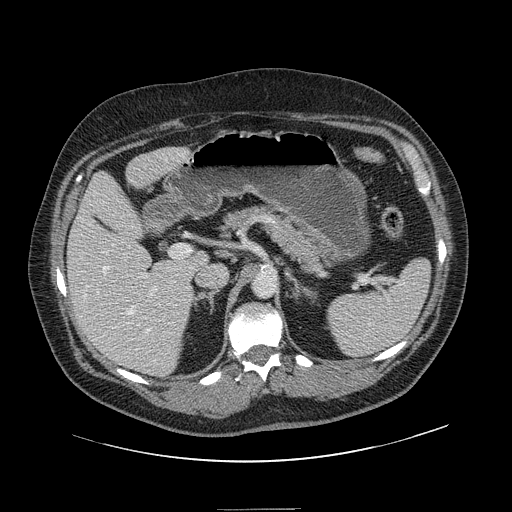
Contrast-enhanced abdominal CT, one axial slice; 120 kVp; intravenous contrast given; soft-tissue window (W 400 / L 40 HU); 2.5 mm slice thickness; 512 × 512 image matrix. Male patient, age 61 years. Case-level facts recorded for this patient, not image findings: diagnosis: colorectal cancer liver metastases, imaged before liver resection; multiple liver metastases: yes; largest metastasis: 2.6 cm.
Outlined on this slice (outlined manually by an expert reader):
- hepatic veins: bounding box <103,244,155,362> (left, top, right, bottom; pixels)
- liver: <68,147,206,376>
- planned liver remnant (the part of the liver to remain after resection): <70,149,207,366>
- portal vein (with intrahepatic branches): <96,251,156,297>